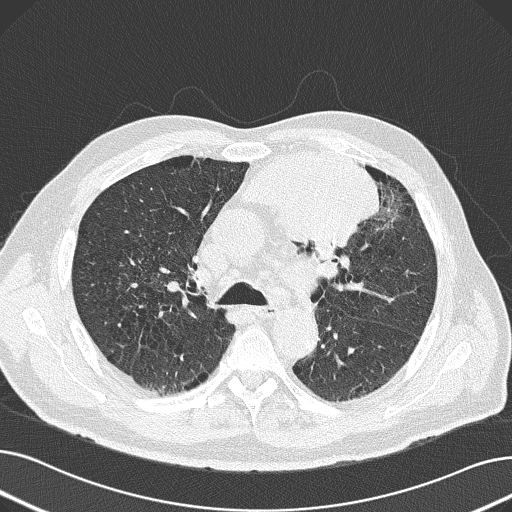
Low-dose screening chest CT, axial slice. Baseline annual screen. Lung window (W 1500 / L -600 HU). 2 mm slice thickness. 120 kVp. Male, age 69 years at enrolment. Former smoker at enrolment.
Lesion marked by an expert reader, box from (x=231, y=140) to (x=382, y=252) px. Reader record for this screening exam (exam-level; its link to the box is not recorded): non-calcified nodule or mass ≥4 mm, left upper lobe, 6 × 10 mm, spiculated (stellate) margins, soft tissue attenuation.